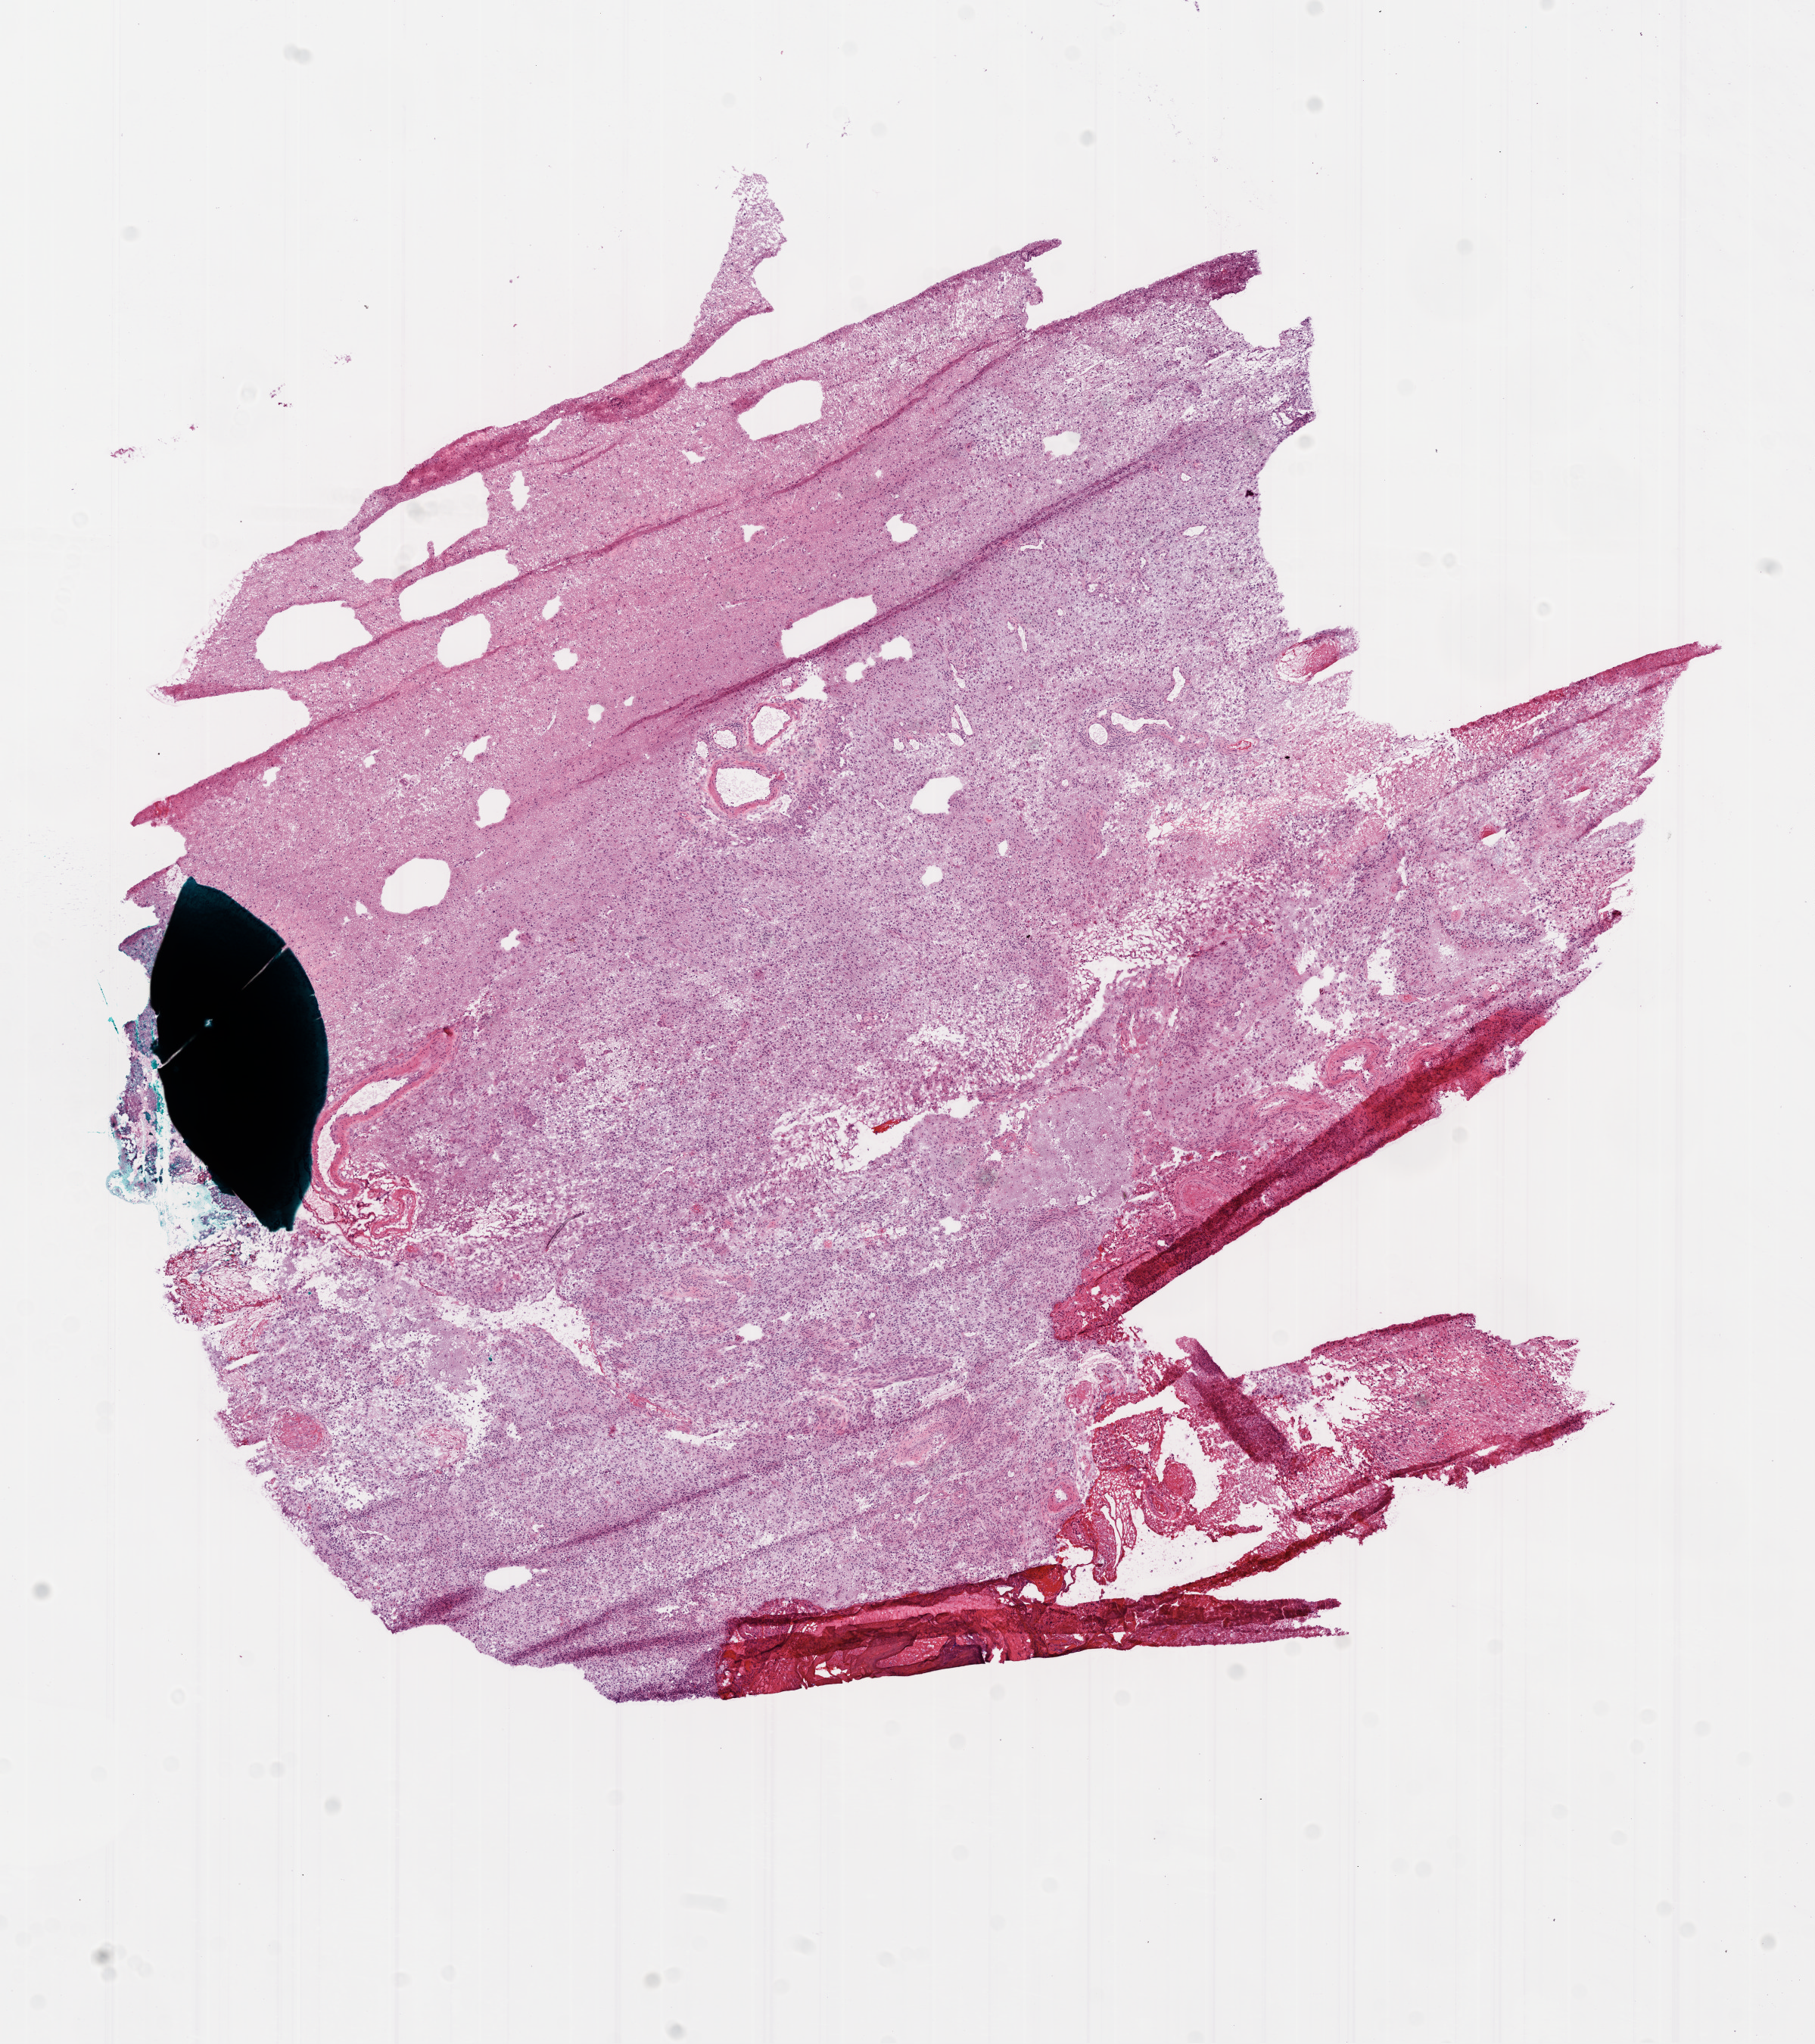
Whole-slide histology image, Hematoxylin and eosin (H&E) stained — shown as a low-resolution overview of the whole scanned area (about 9.7 x 10.9 mm, slide scanned at 20x), frozen section from the bottom of the tissue portion, brain, primary tumour sample. Female, age 55 years at initial diagnosis. Composition of this section per pathologist review: tumour cells 70%, tumour nuclei 95%, normal cells 0%, stromal cells 20%, necrosis 10%.
Diagnosis: Glioblastoma.